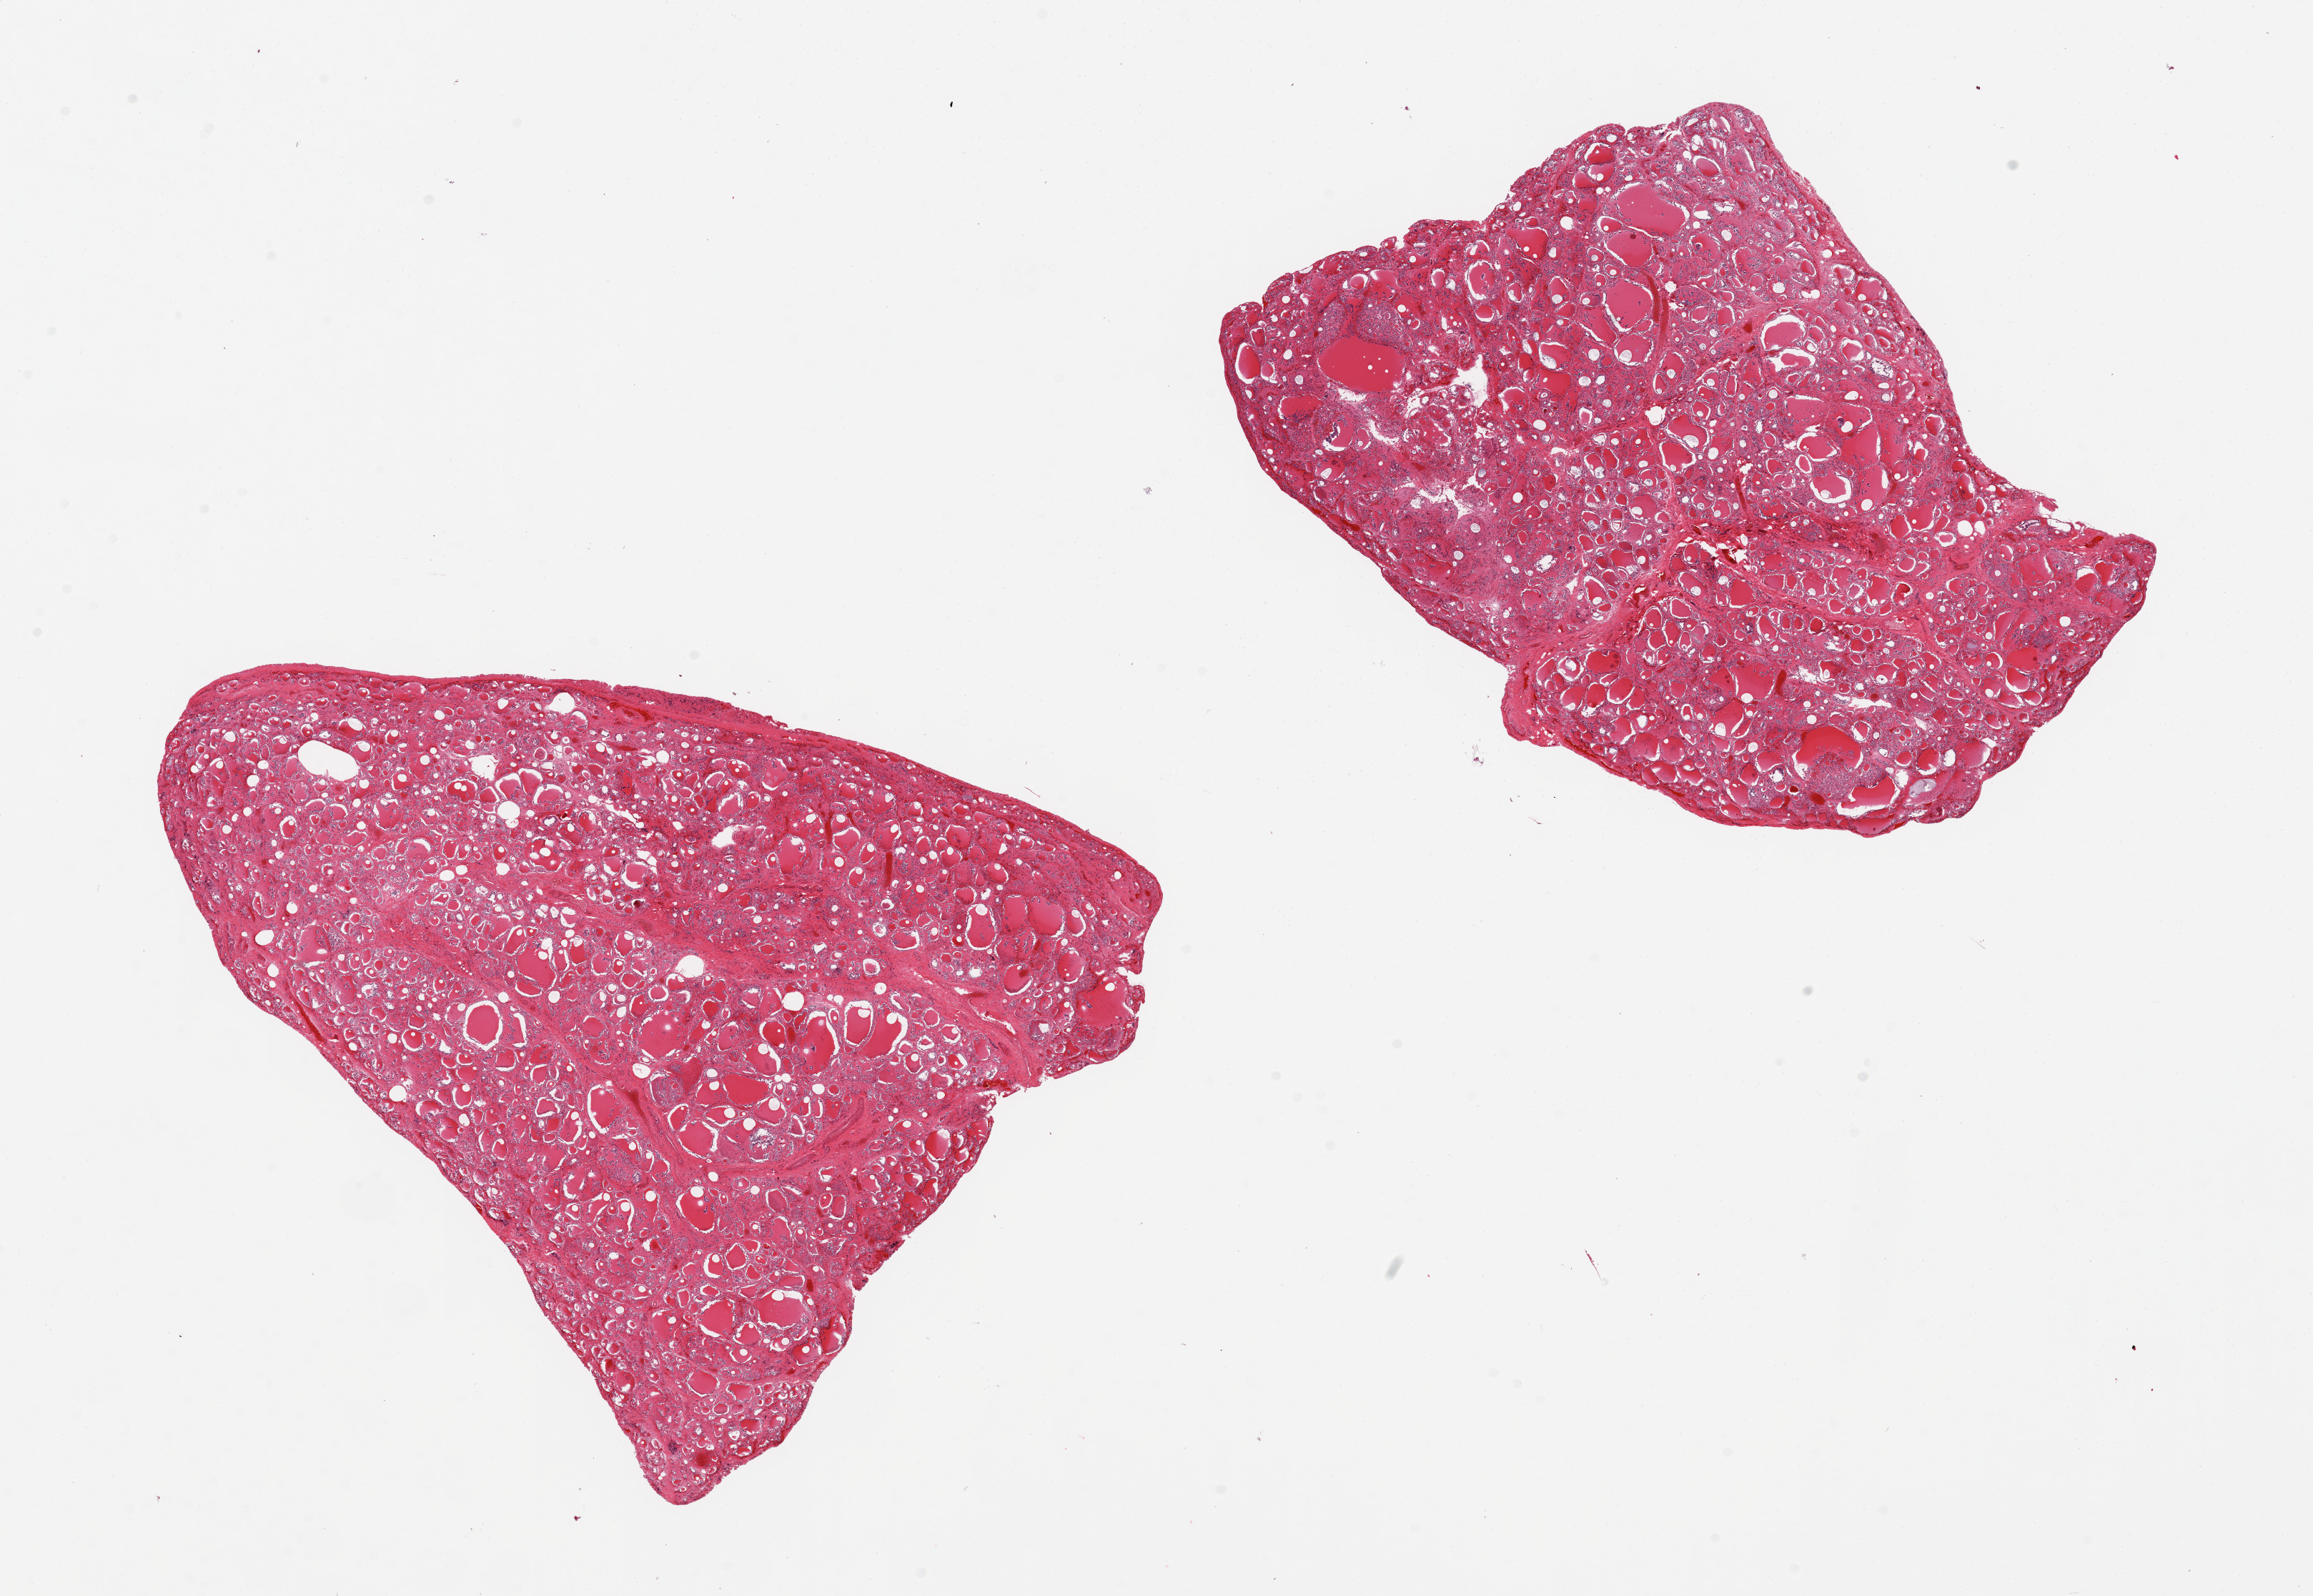
Whole-slide image, hematoxylin and eosin (H&E) stain — low-resolution overview of the scanned area, about 25.6 x 17.7 mm, PAXgene-fixed paraffin-embedded (PFPE) section, sampled site (target tissue): thyroid, donor tissue sample.
Review note (as recorded): 2 pieces; nodular.